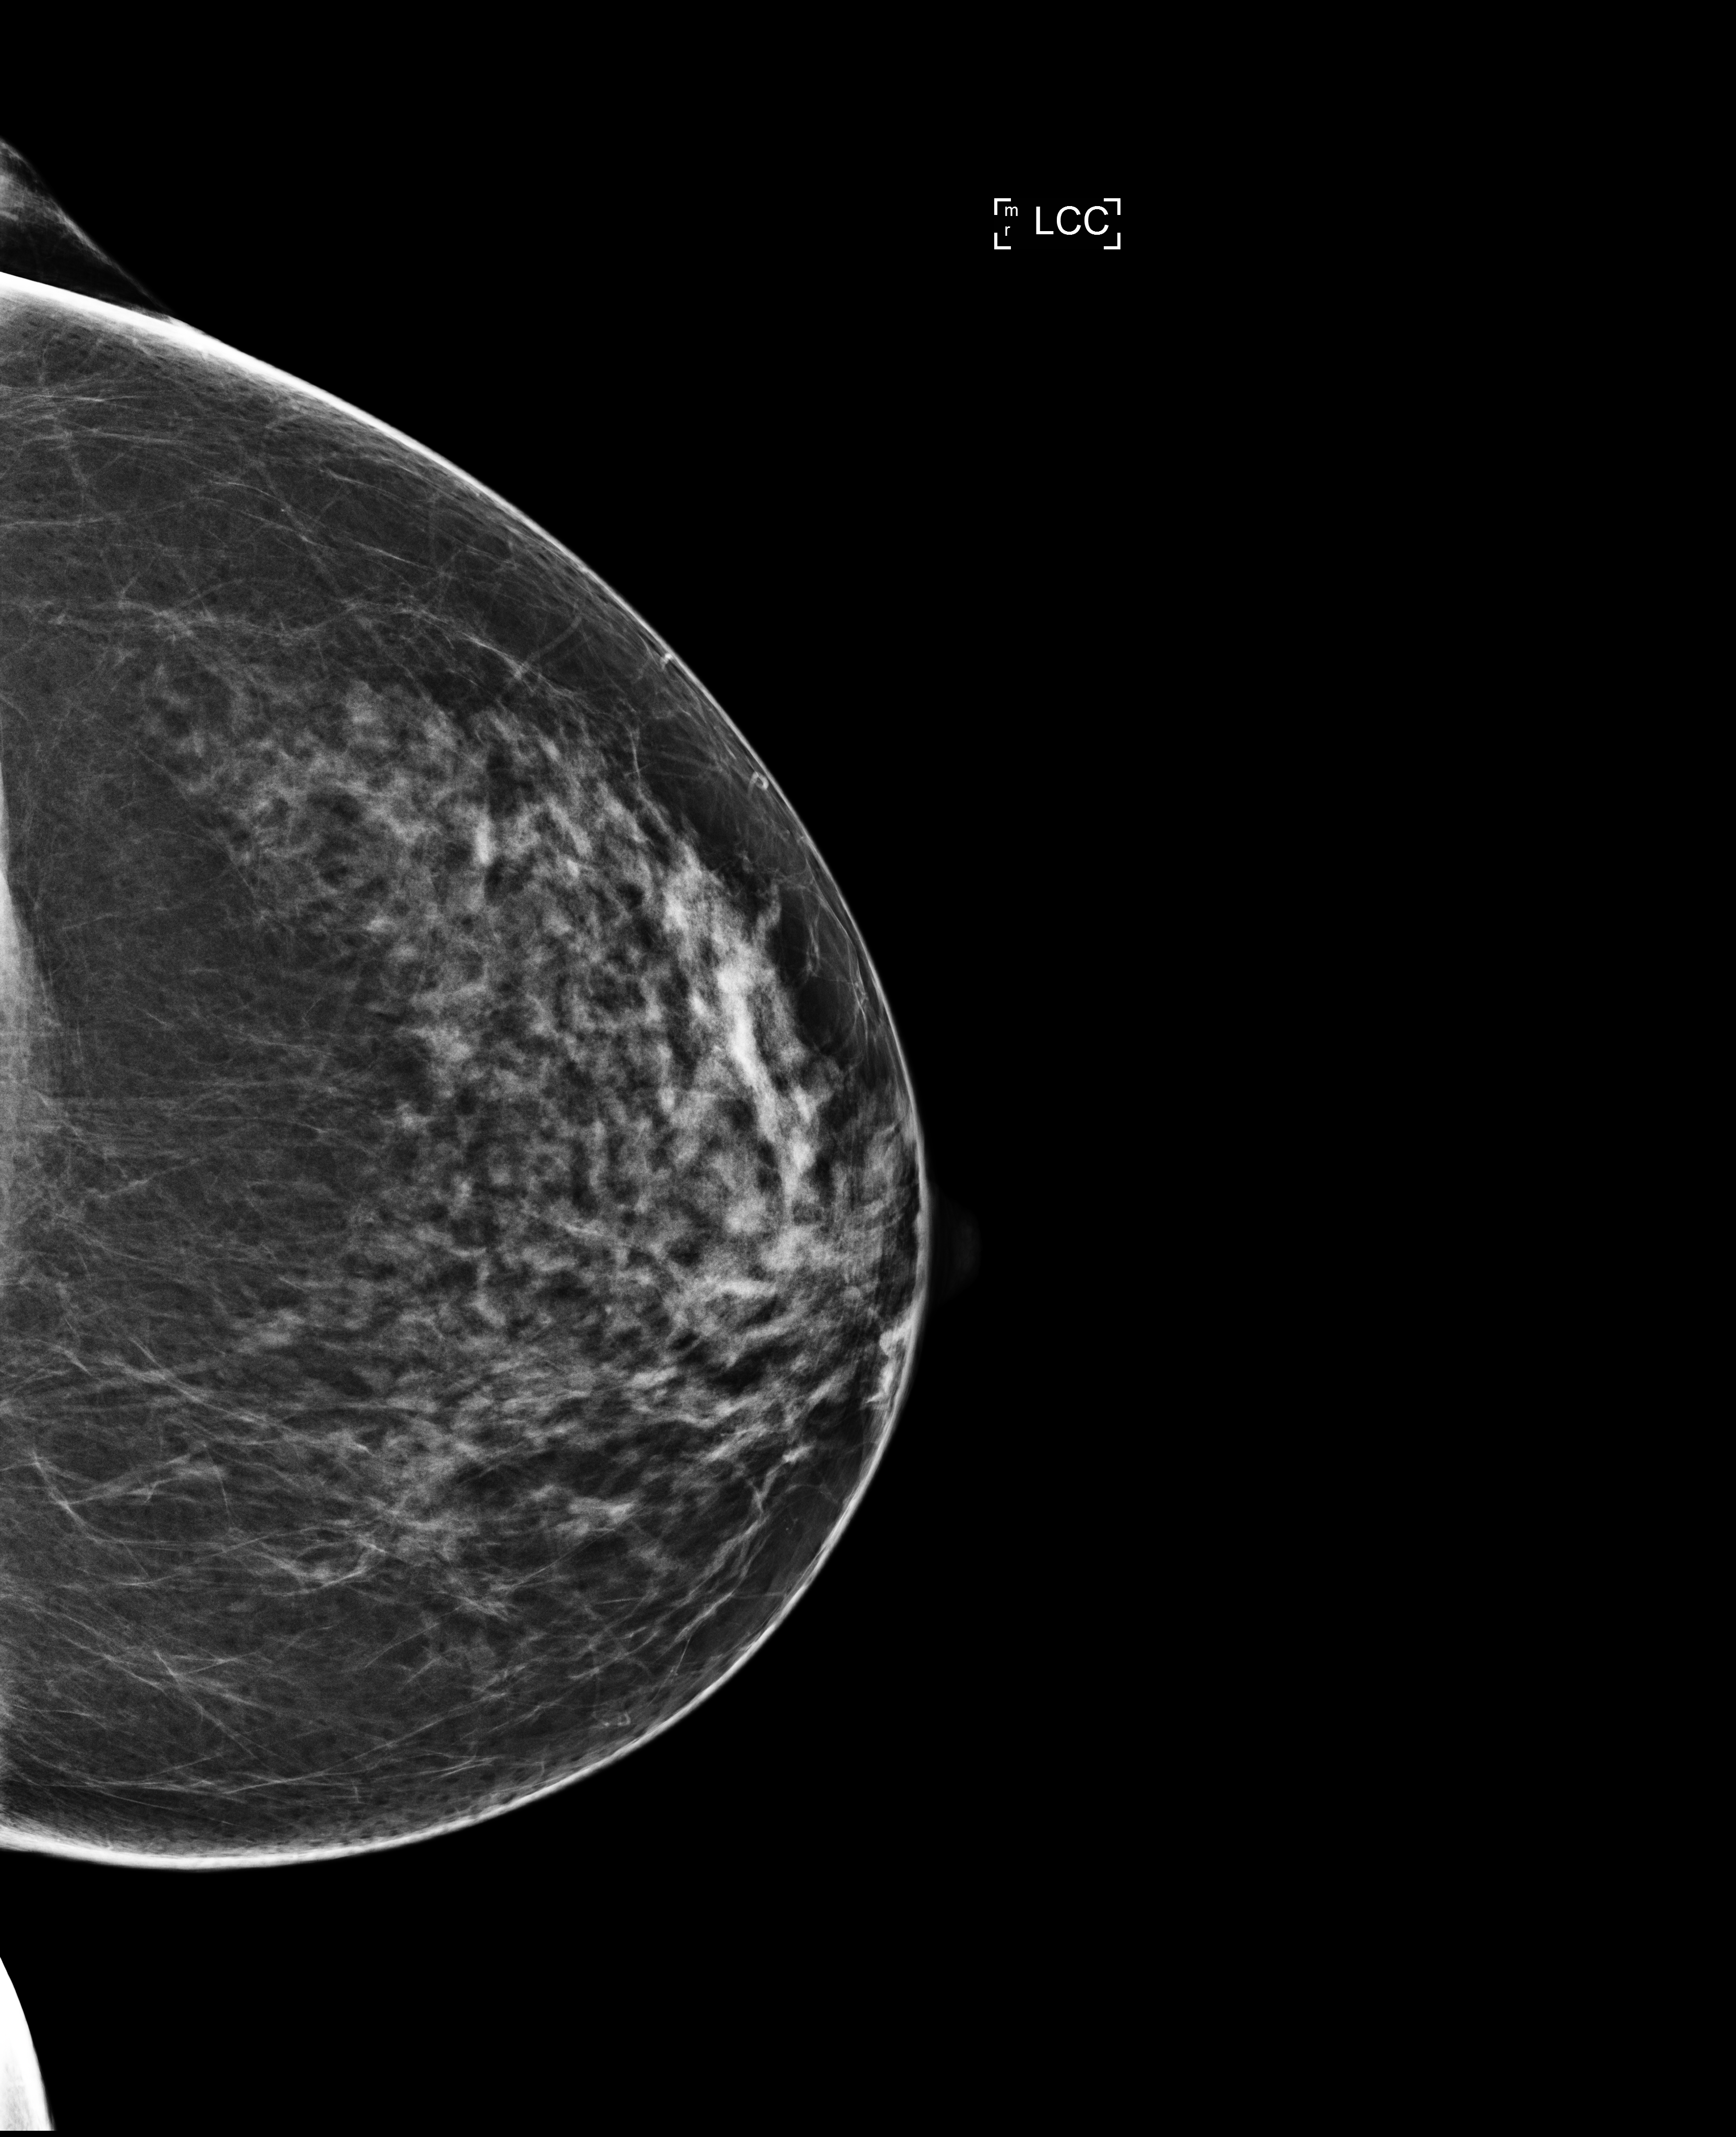
Screening examination; compressed breast thickness 73 mm. Patient: female, 53 years.
Image type: full-field digital mammogram. Breast: left. Projection: cranio-caudal projection.